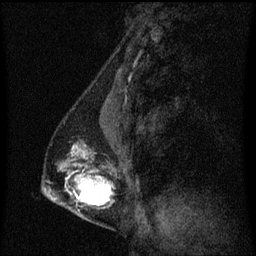
Breast MRI (dynamic contrast-enhanced), one sagittal slice; position 26 of 60 along the scan axis; dynamic contrast-enhanced series, image 2 of 3 at this slice position (ordered by acquisition); 1.5 T; TE 4.2 ms, TR 8.4 ms; 256 × 256 image matrix, field of view 200 × 200 mm. Female patient, age 40 years. From the clinical record (not read from this slice): setting: breast cancer imaged before/during neoadjuvant chemotherapy; receptor status: triple-negative.
Structures marked on this image (semi-automatic segmentation, software-assisted and operator-edited):
- analysis volume of interest (the breast-tissue region the enhancement analysis was run in; not a lesion): bounding box (x1, y1, x2, y2) in pixels: (44, 128, 120, 221)
- tumour enhancement mask (voxels above the 70 % enhancement threshold inside the analysis volume of interest): (68, 148, 113, 207)